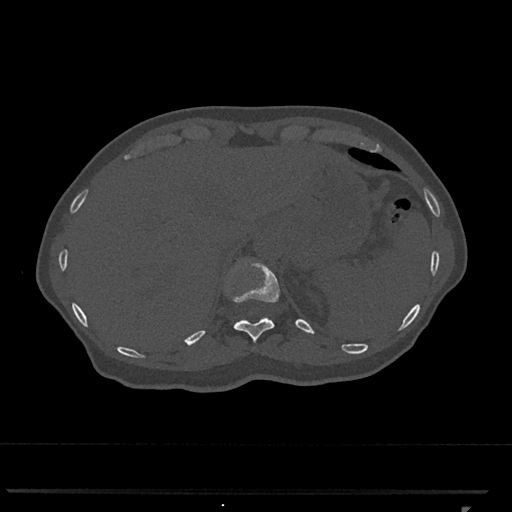
CT including the spine, one axial slice; slice 508 of 793 in the series (ordered by position); reconstruction kernel Br40s/3; 120 kVp; bone window (W 1800 / L 400 HU); 0.5 mm slice thickness; 512 × 512 image matrix, field of view 380 × 380 mm. Patient: female, 62 years. Case-level facts recorded for this patient, not image findings: primary cancer: renal.
Annotated regions visible in this slice (semi-automatic segmentation, software-assisted and operator-edited):
- T11 vertebra: bounding box (x1, y1, x2, y2) in pixels: (233, 260, 280, 343)